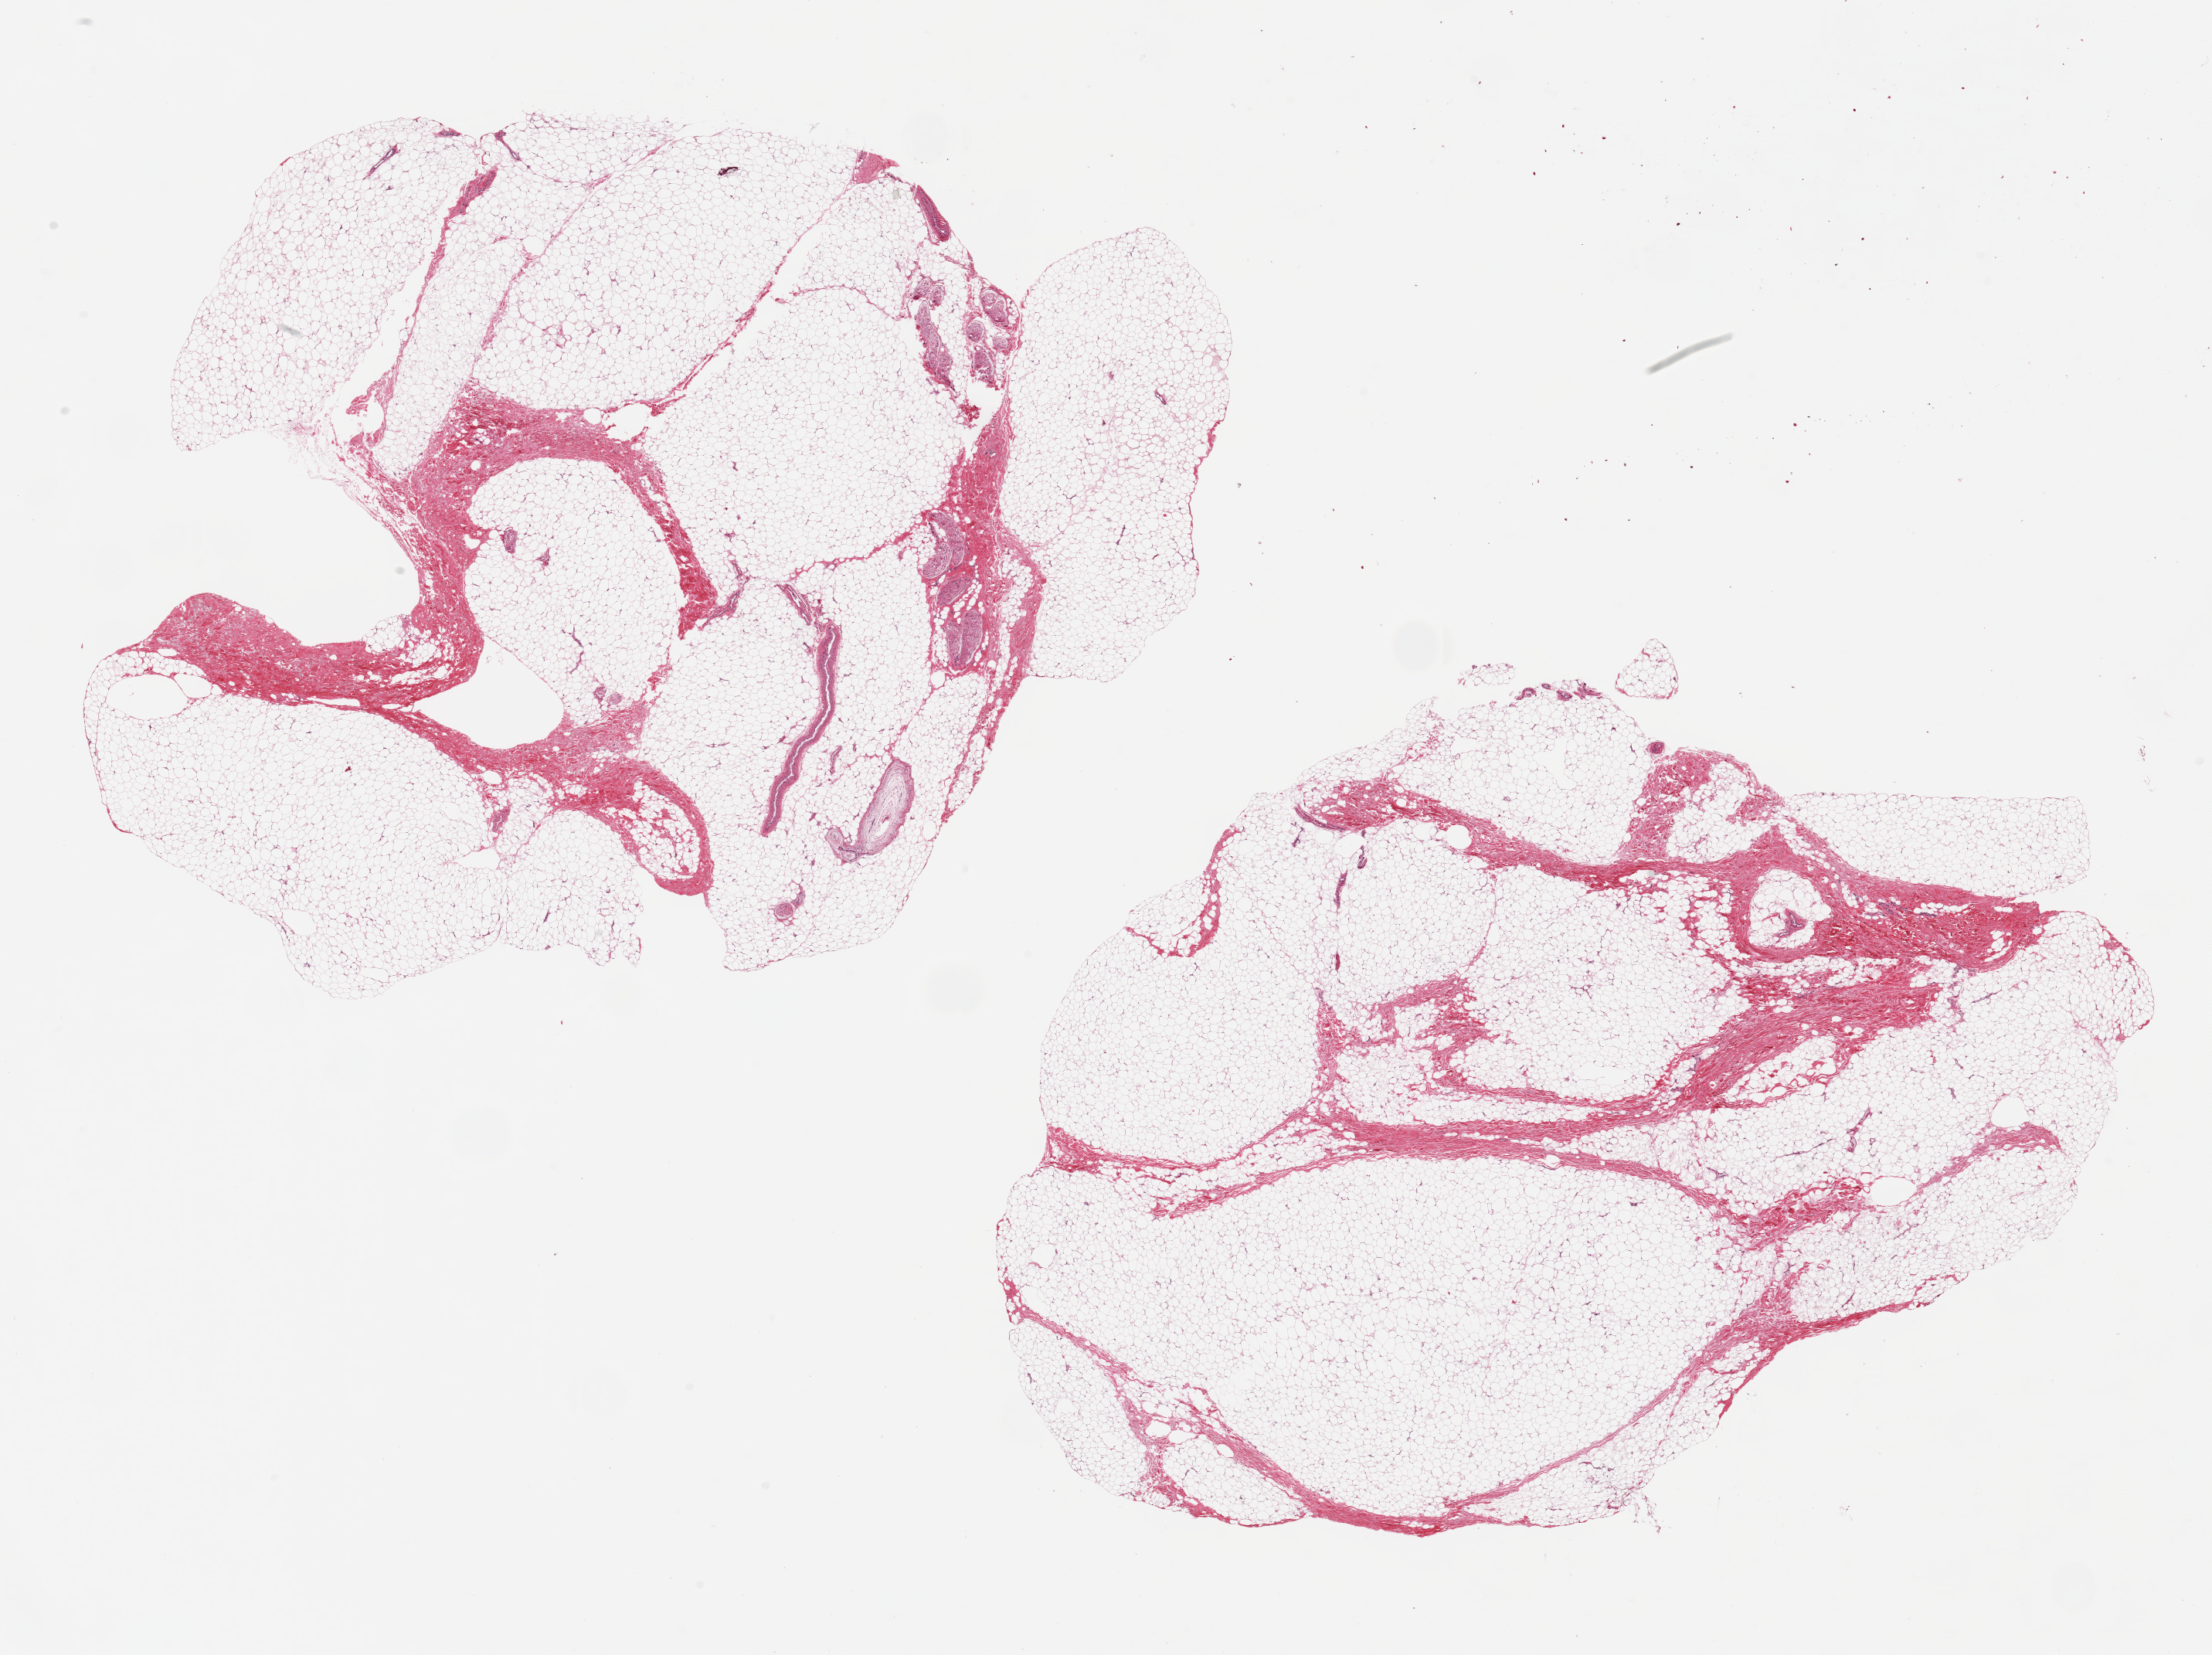
Whole-slide image, hematoxylin and eosin (H&E) stain, brightfield — shown as a low-resolution overview of the whole scanned area (about 22.6 x 16.9 mm), PAXgene-fixed paraffin-embedded (PFPE) section, section of breast (target tissue), tissue donor sample. Male donor.
Review note (as recorded): 2 ~11x8mm aliquots, all adipose + fibrous tissue, no mammary ductal elements.